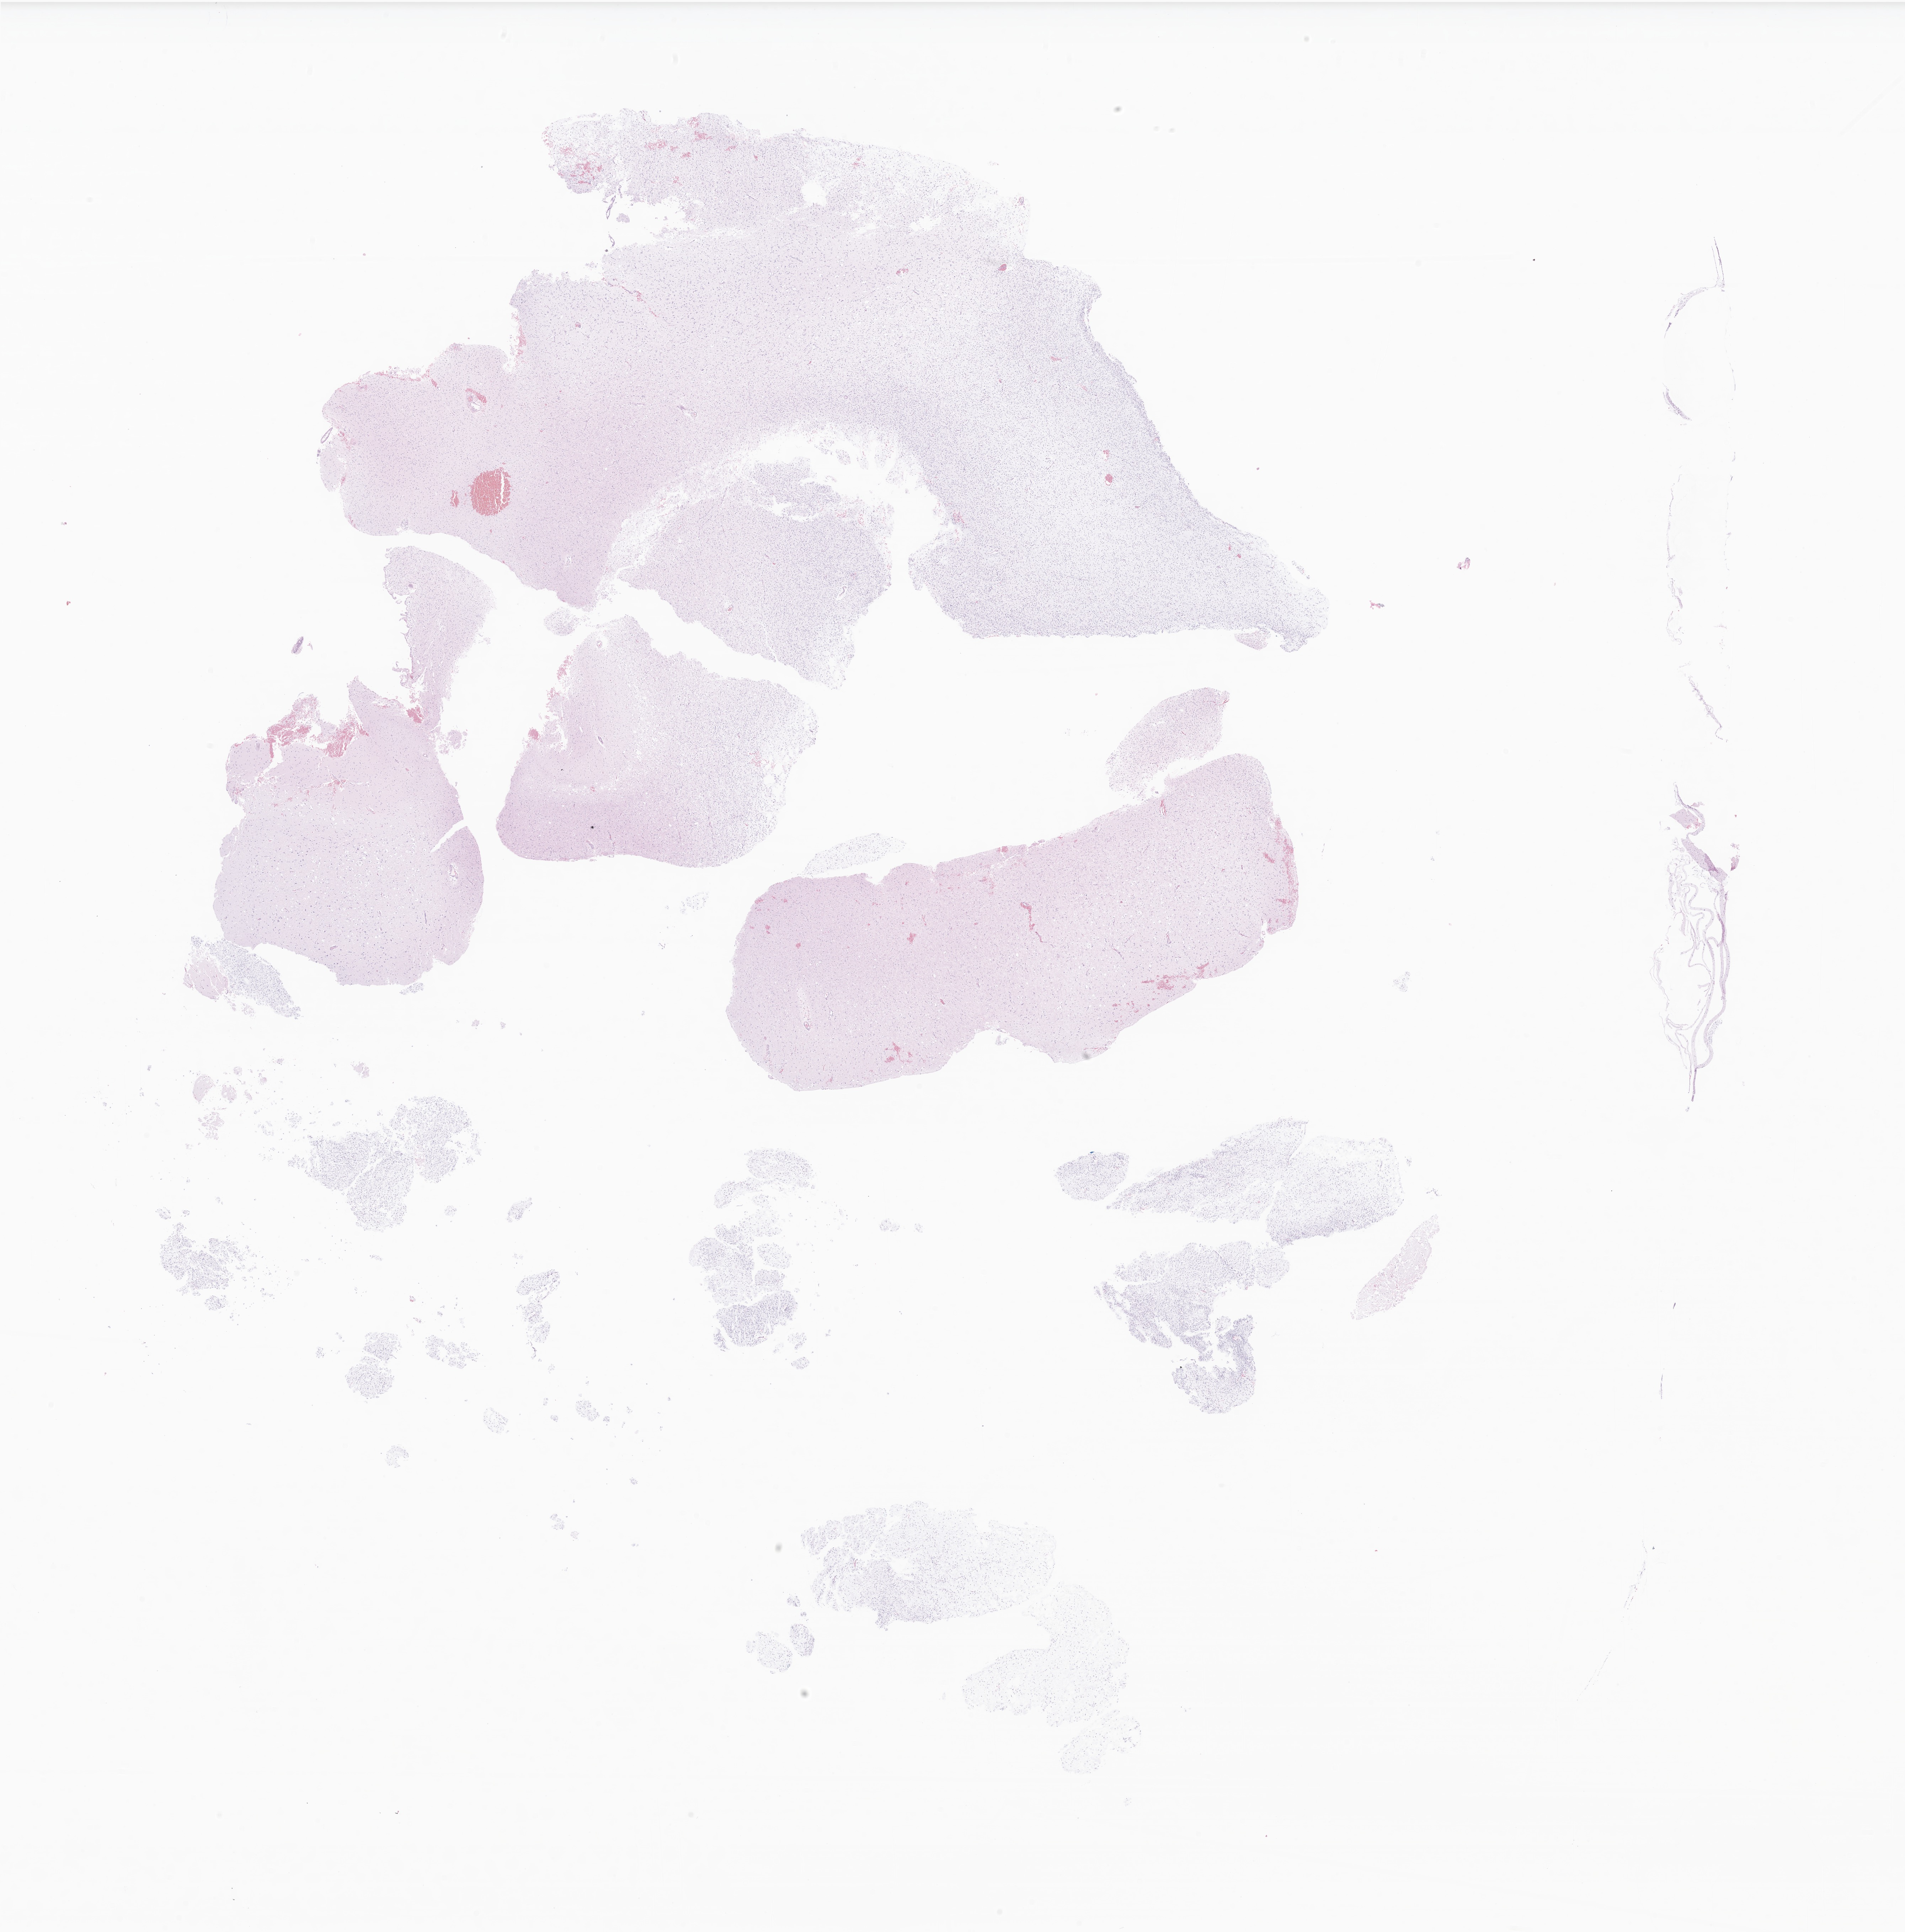
Haematoxylin and eosin whole-slide image of tumor tissue from the frontal lobe, low-resolution overview of the scanned area, about 22.6 x 22.9 mm; formalin-fixed, paraffin-embedded (FFPE) tissue. Patient female; age 47 months (3 years 11 months).
* diagnosis: Glioma, malignant